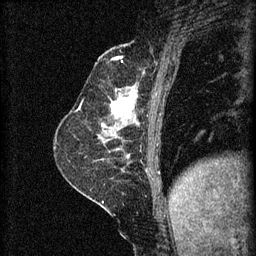
Breast MRI (dynamic contrast-enhanced), one sagittal slice. Position 23 of 60 along the scan axis. 3 images stored at this slice position (order not interpretable as contrast timing). 1.5 T. TE 4.2 ms, TR 8.2 ms. 2 mm slice thickness. 256 × 256 image matrix. Female patient, age 59 years.
Outlined on this slice (semi-automatically segmented with operator editing):
- analysis volume of interest (the breast-tissue region the enhancement analysis was run in; not a lesion): bounding box (x1, y1, x2, y2) in pixels: (98, 92, 137, 135)
- tumour enhancement mask (voxels above the 70 % enhancement threshold inside the analysis volume of interest): (112, 94, 137, 119)